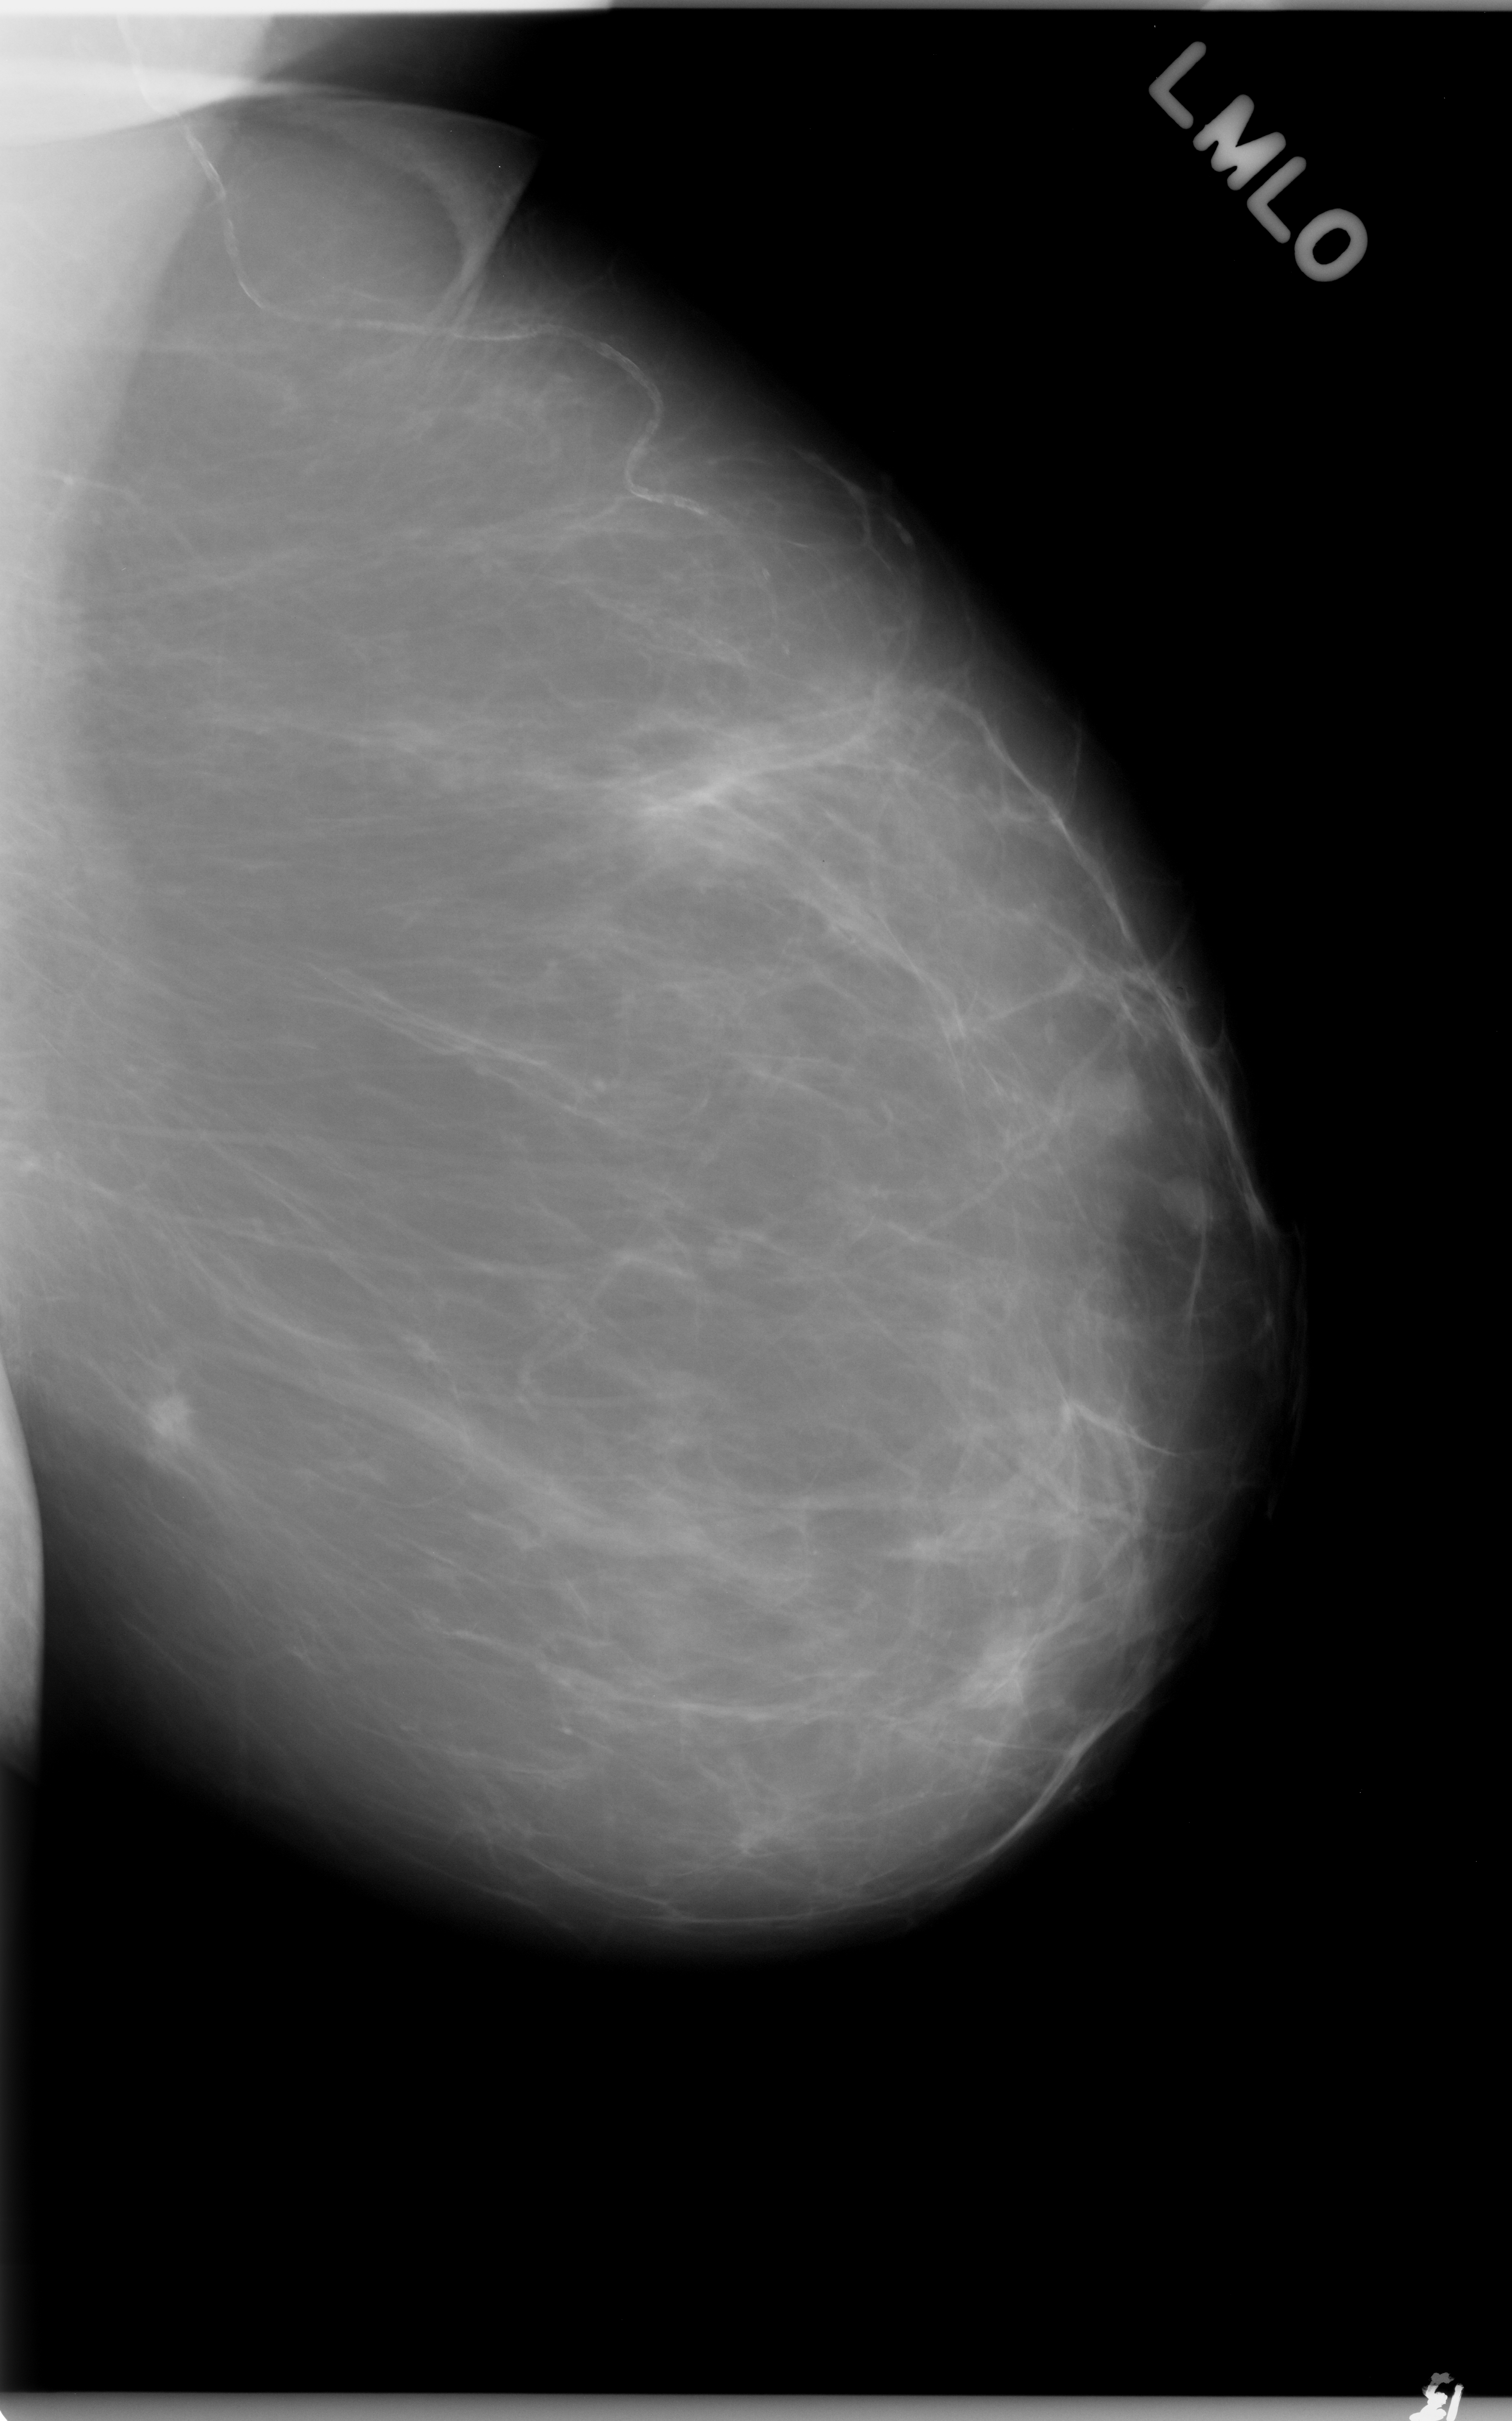
Scanned film-screen mammogram; left breast; MLO view; BI-RADS breast density category 1 (scale 1–4); 1512 × 2421 image matrix.
Expert-marked regions of interest on this film, with their recorded descriptors:
- mass, shape irregular, margins spiculated; BI-RADS assessment category 5; subtlety rating 5 on a 1 (subtle) to 5 (obvious) scale; pathology (as recorded): malignant: box from (x=110, y=1363) to (x=214, y=1484) px